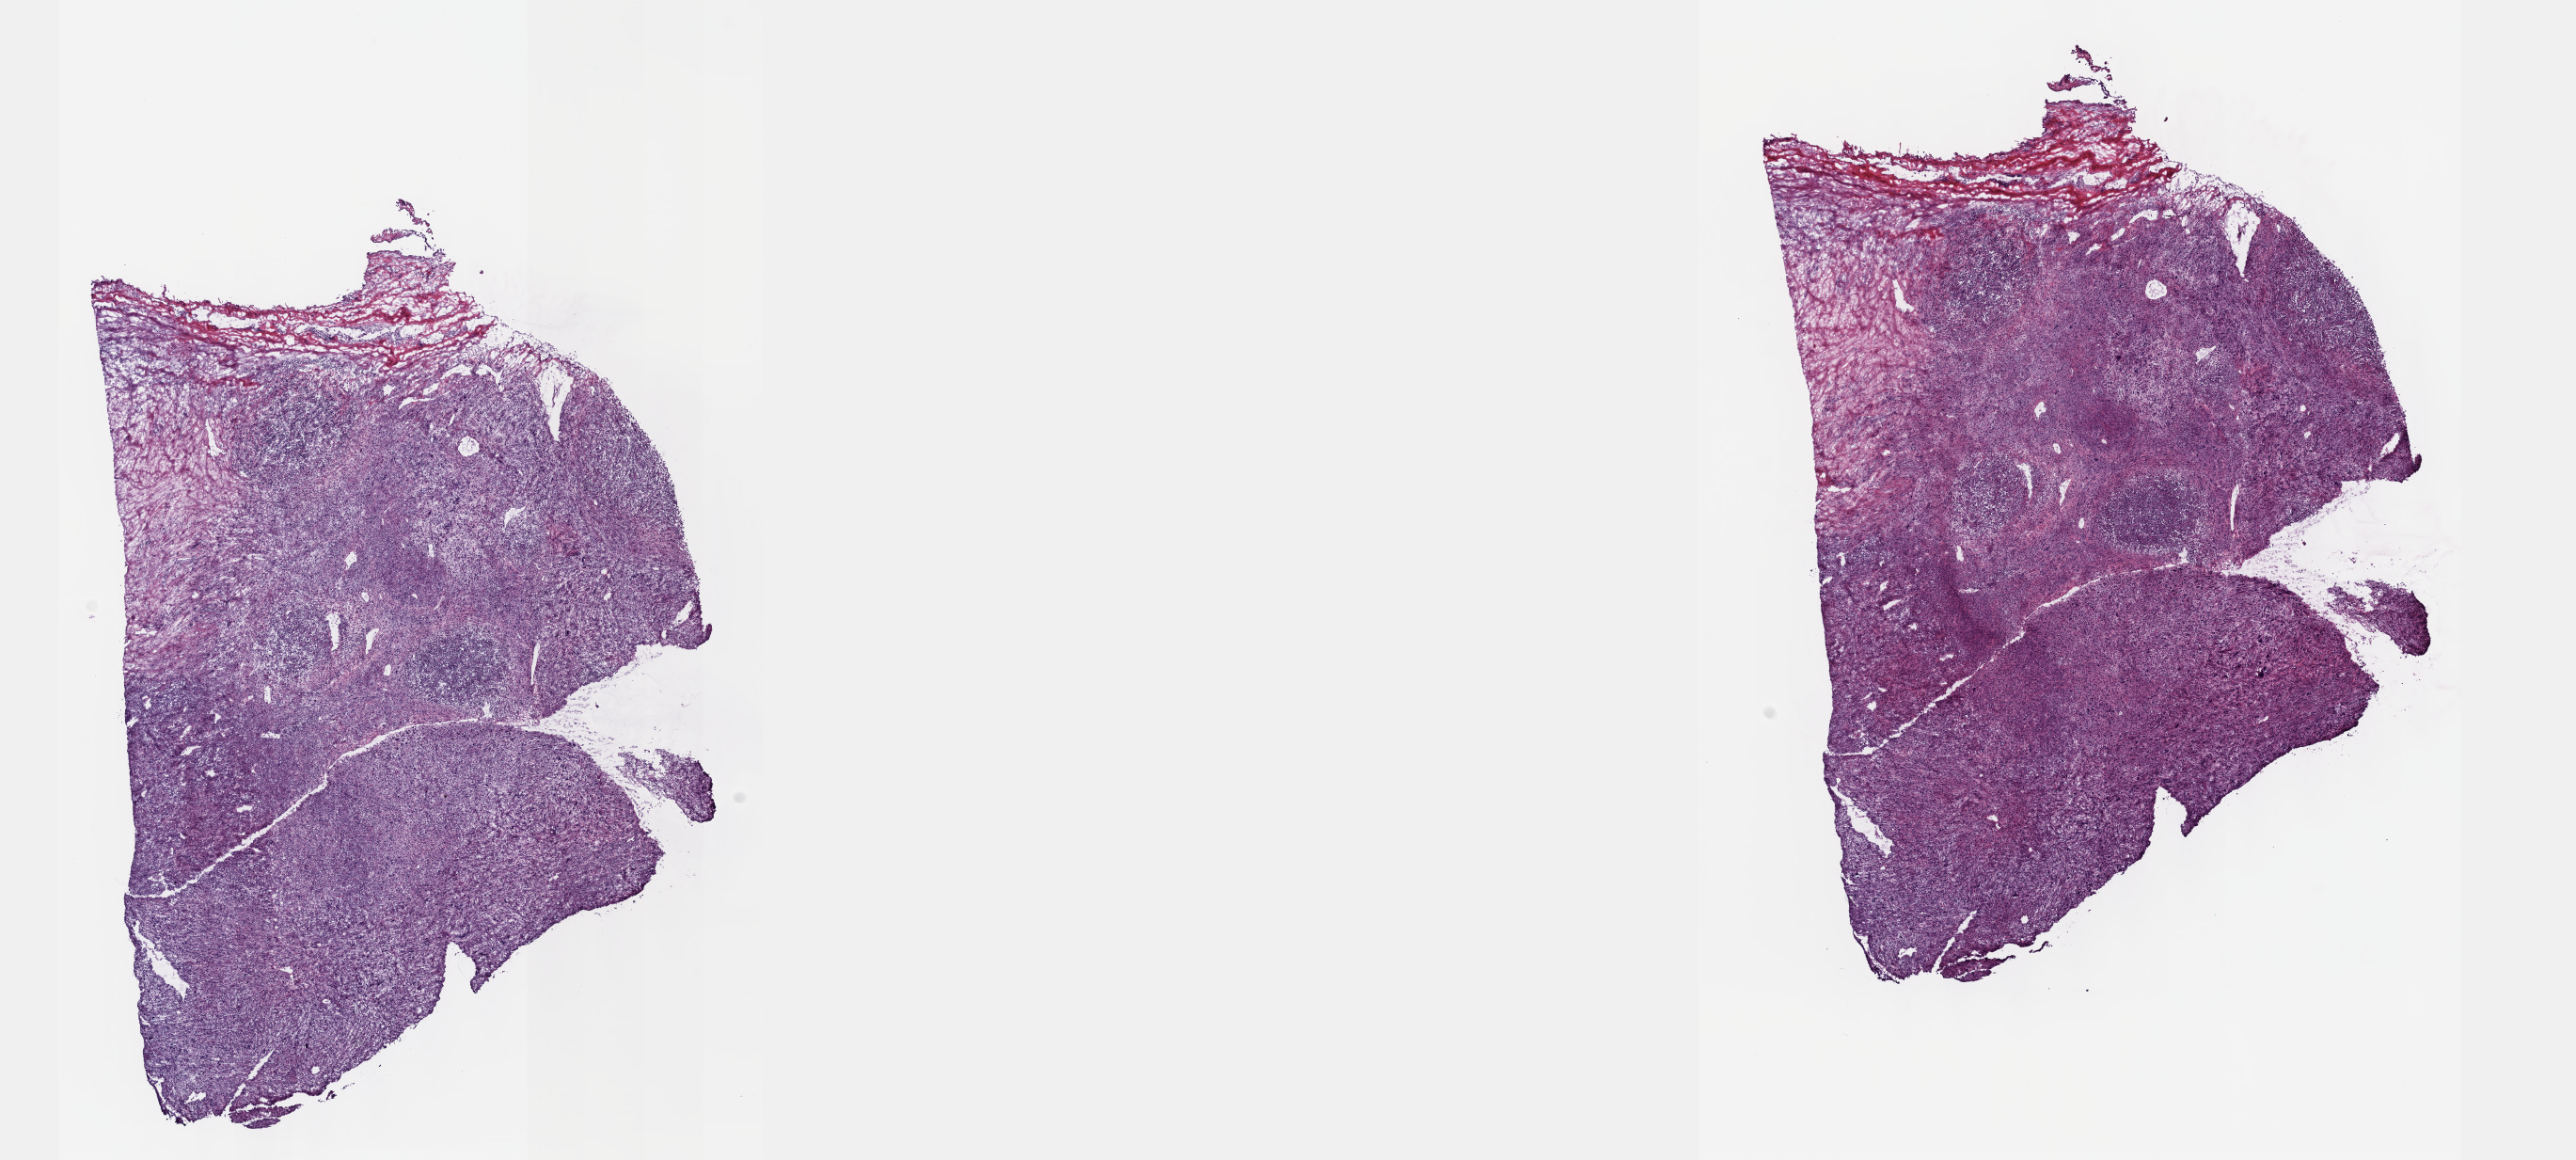
Digitized H&E tissue section (whole slide), a low-resolution overview of the entire scanned area, about 22.1 x 10.0 mm; frozen section; primary tumour sample from the connective, subcutaneous and other soft tissues. Male, age 51 years at initial diagnosis. Pathologist review of this section (percent, as recorded): tumour cells 100%, tumour nuclei 75%, normal cells 0%, stromal cells 0%, necrosis 0%. Infiltration values recorded for this section: lymphocyte infiltration 1%, monocyte infiltration 0%, neutrophil infiltration 0%.
Diagnosis: Fibromyxosarcoma (connective, subcutaneous and other soft tissues of thorax).